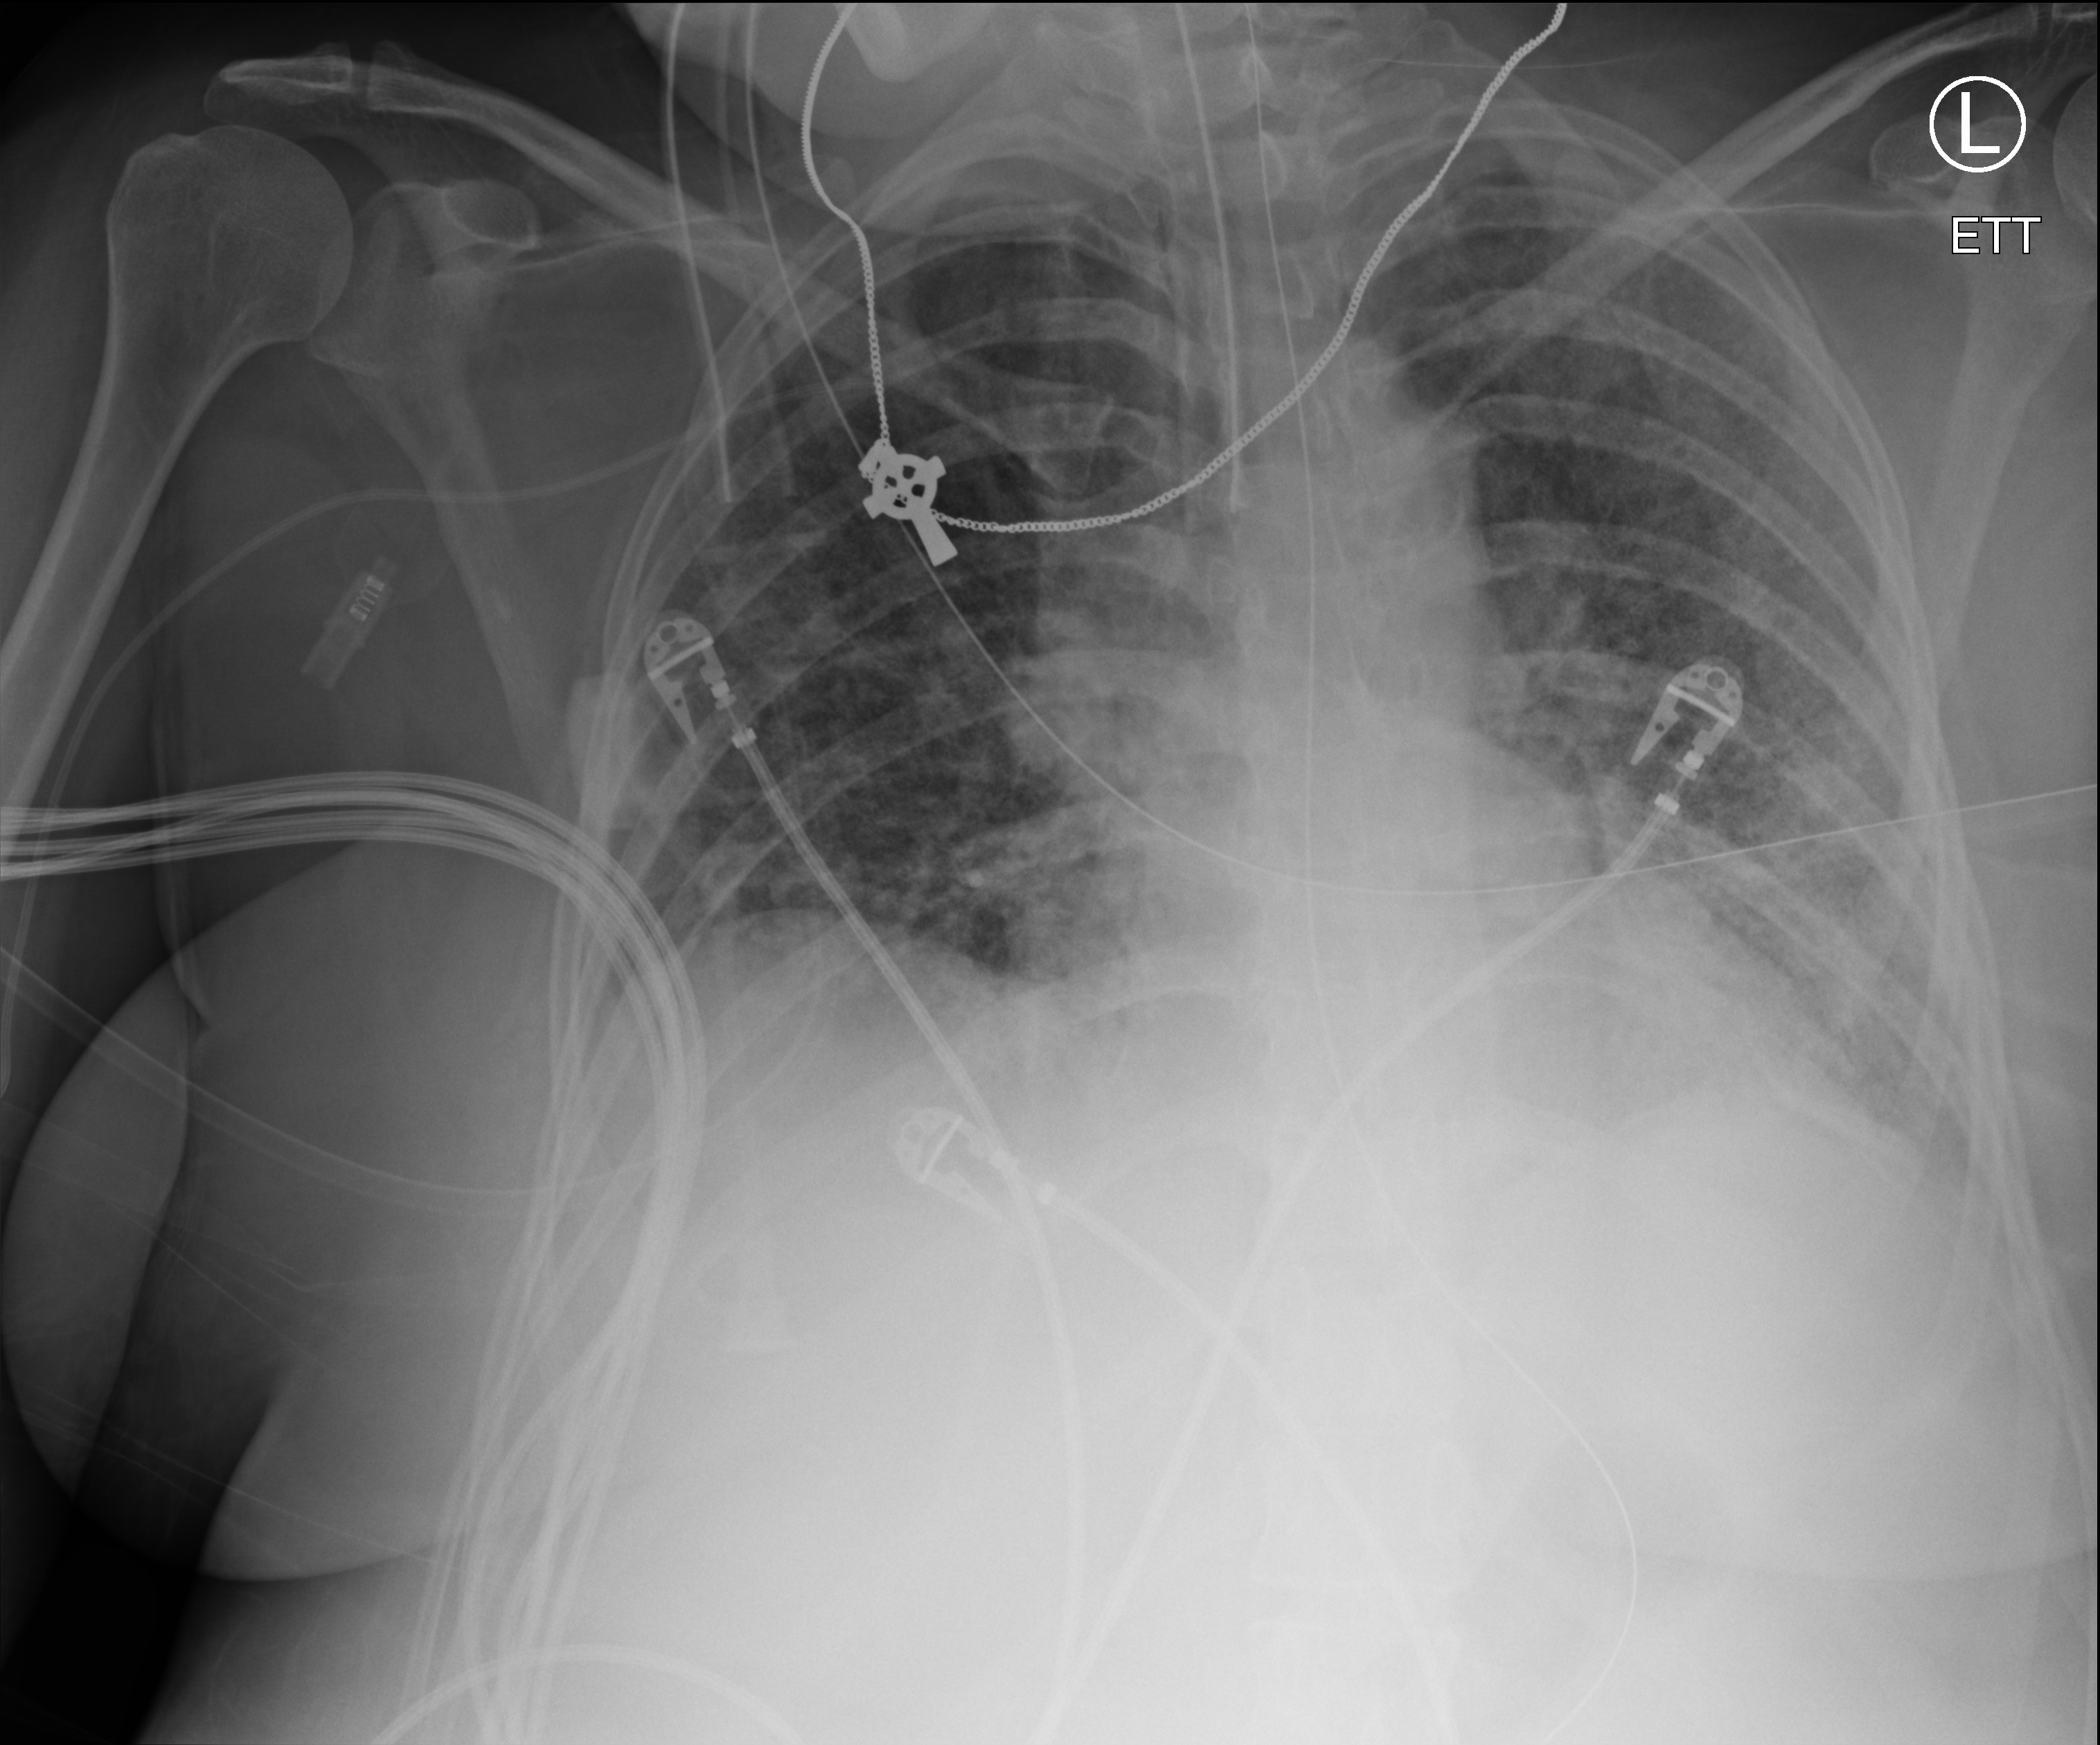
Bedside chest radiograph (computed radiography); anteroposterior (AP) projection. Female patient hospitalised with COVID-19, age 18–59 years.
From the hospital-stay record, not from the radiograph (when in the stay this image was taken is not recorded):
- admitted to intensive care during this hospital stay: yes